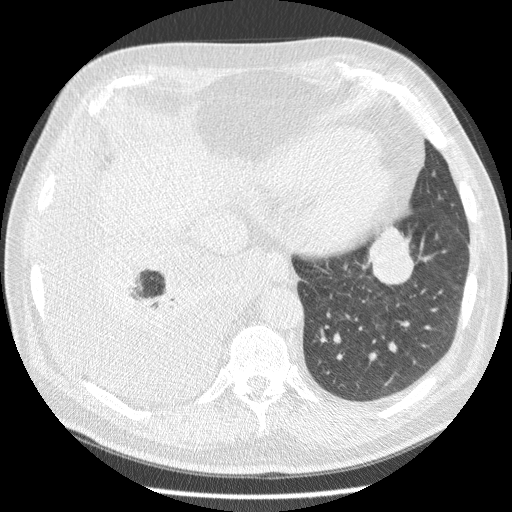
Low-dose screening chest CT, one axial slice; 120 kVp; lung window (W 1500 / L -600 HU); 512 × 512 image matrix.
Annotated regions visible in this slice (expert manual segmentation):
- lesion 1 (tumor, lower lobe of left lung): box from (x=367, y=227) to (x=421, y=284) px